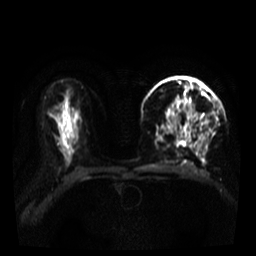
Breast MRI, one axial slice; position 22 of 39 along the scan axis; diffusion-weighted series; image 2 of 4 stored at this slice position (different b-values; order by instance number); 3 T; 5 mm slice thickness; 256 × 256 image matrix, field of view 320 × 320 mm. Female patient.
Outlined on this slice (manually delineated by an expert):
- tumour on diffusion-weighted imaging: box from (x=170, y=98) to (x=202, y=120) px